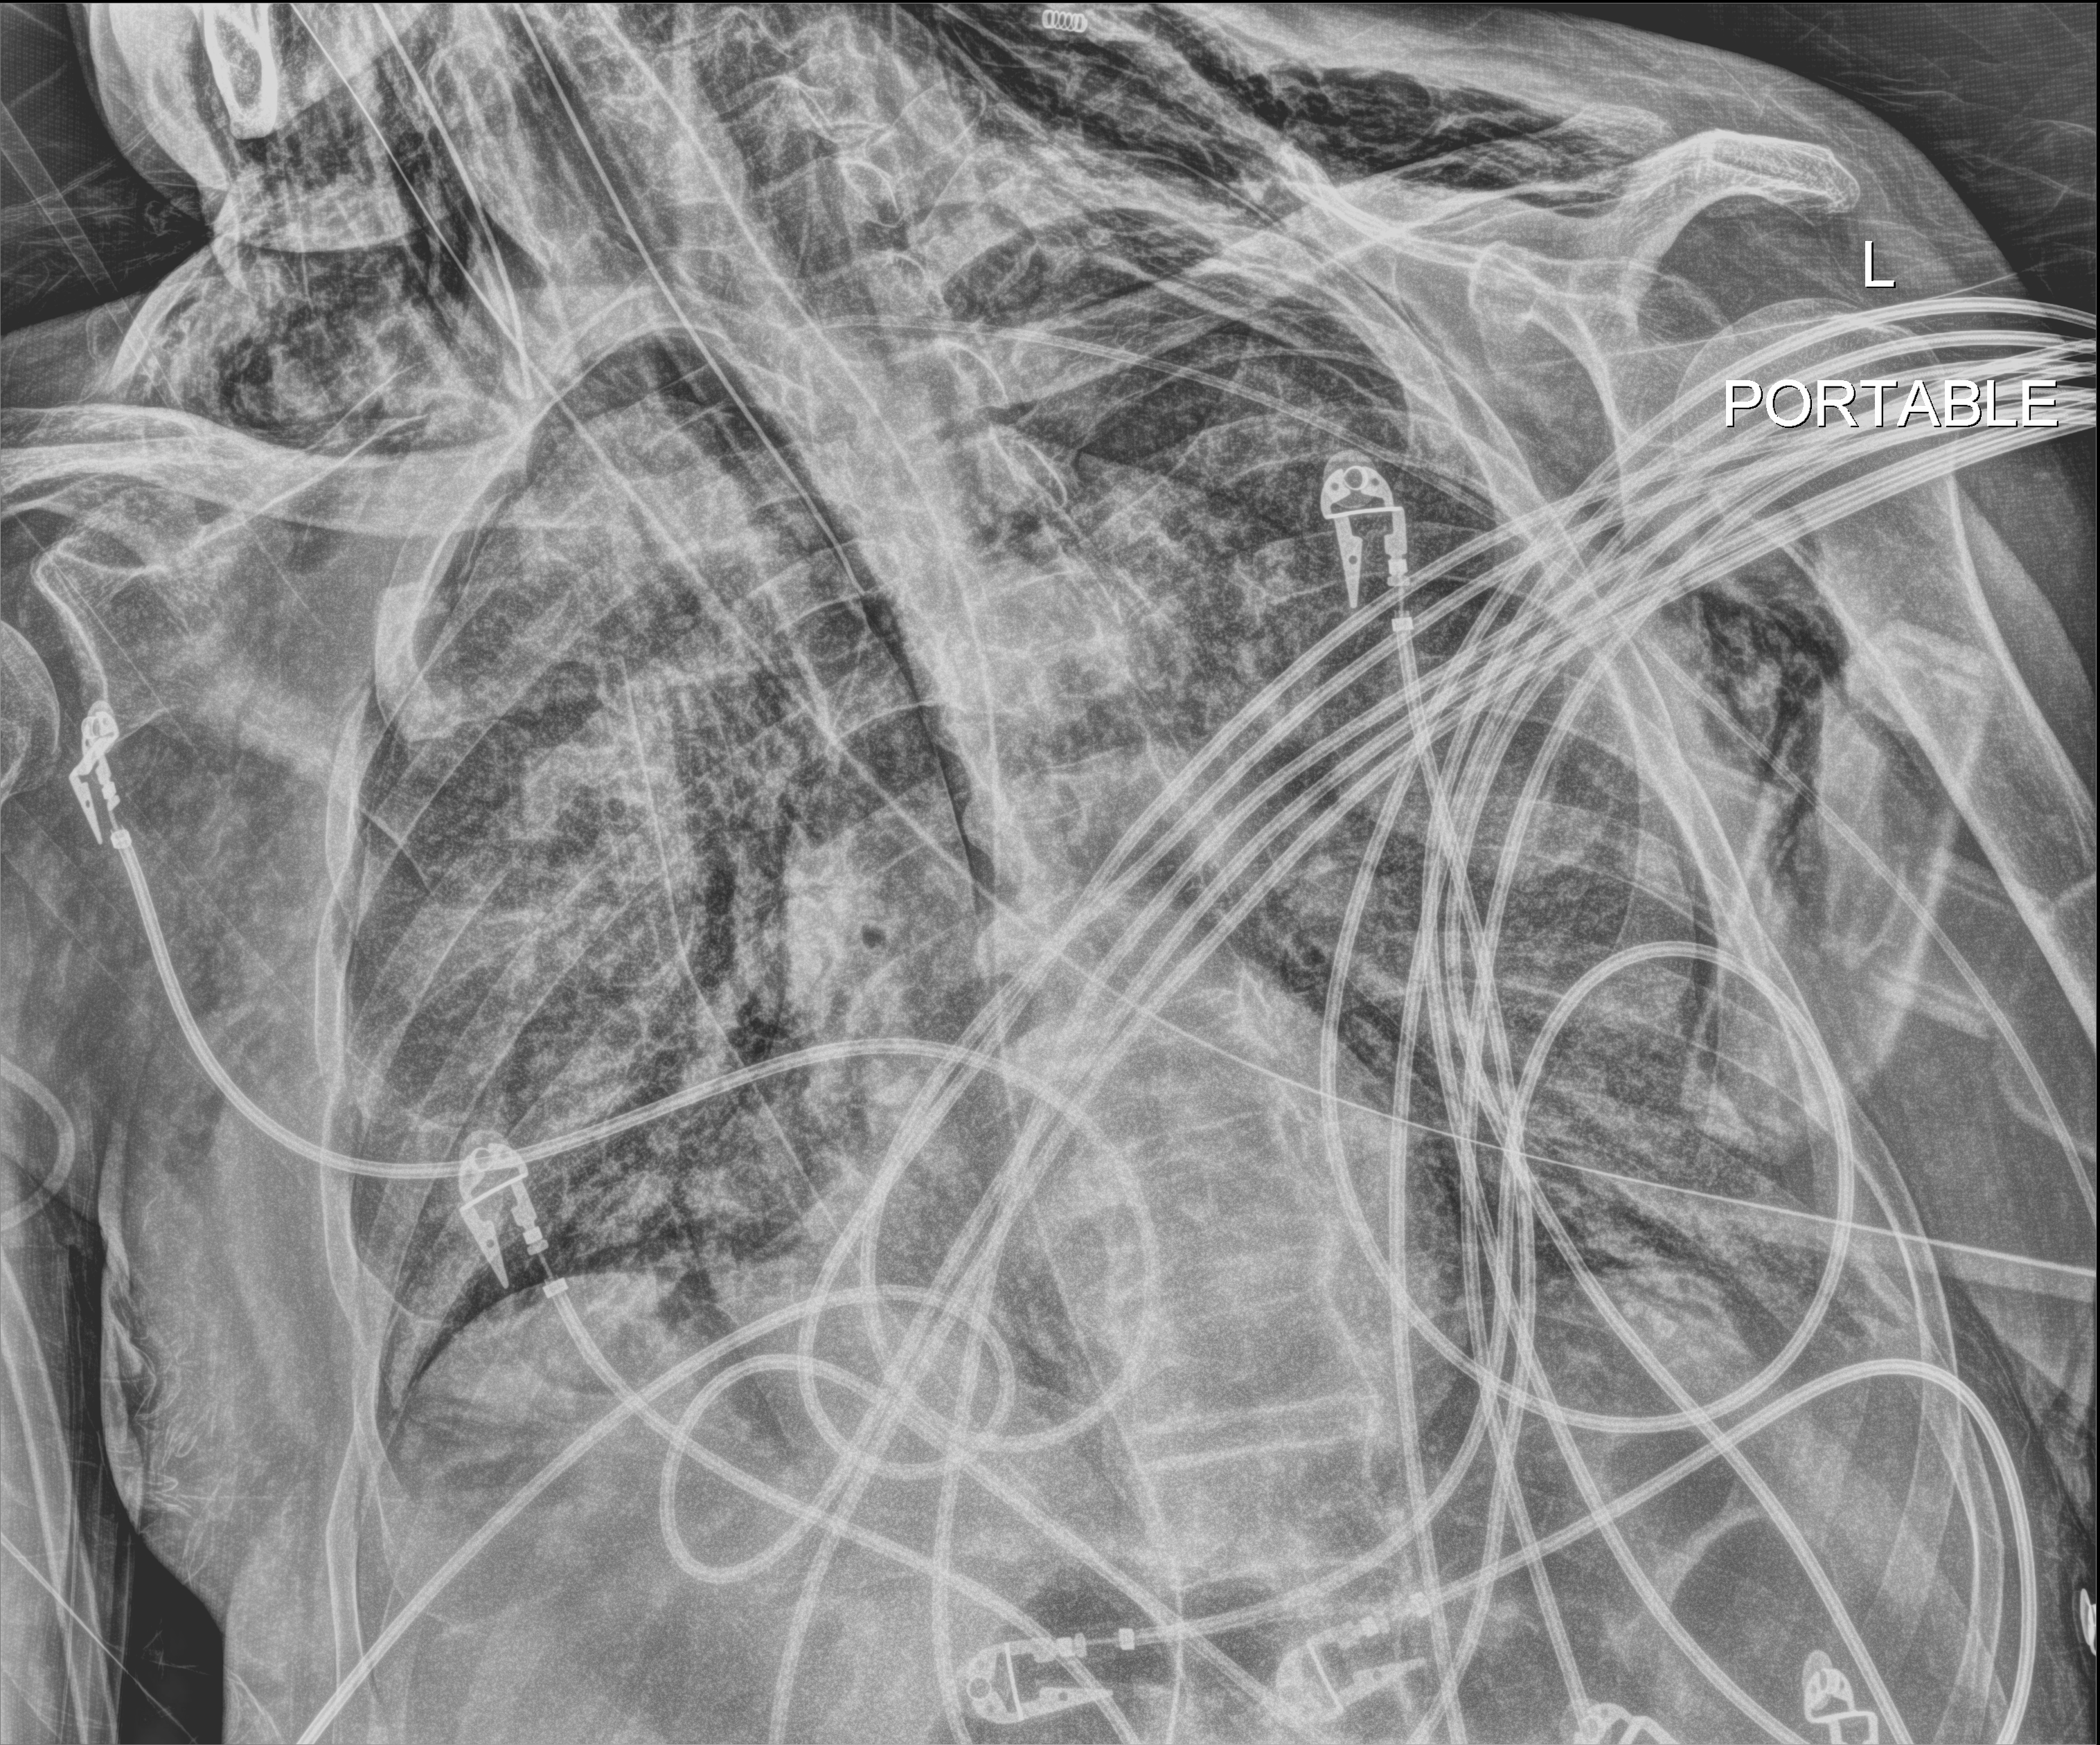
Bedside chest radiograph (digital radiography). Male patient hospitalised with COVID-19, age 75–90 years.
From the hospital-stay record, not from the radiograph (when in the stay this image was taken is not recorded): chronic kidney disease (admission record): no; mechanically ventilated during this hospital stay: yes; admitted to intensive care during this hospital stay: yes.